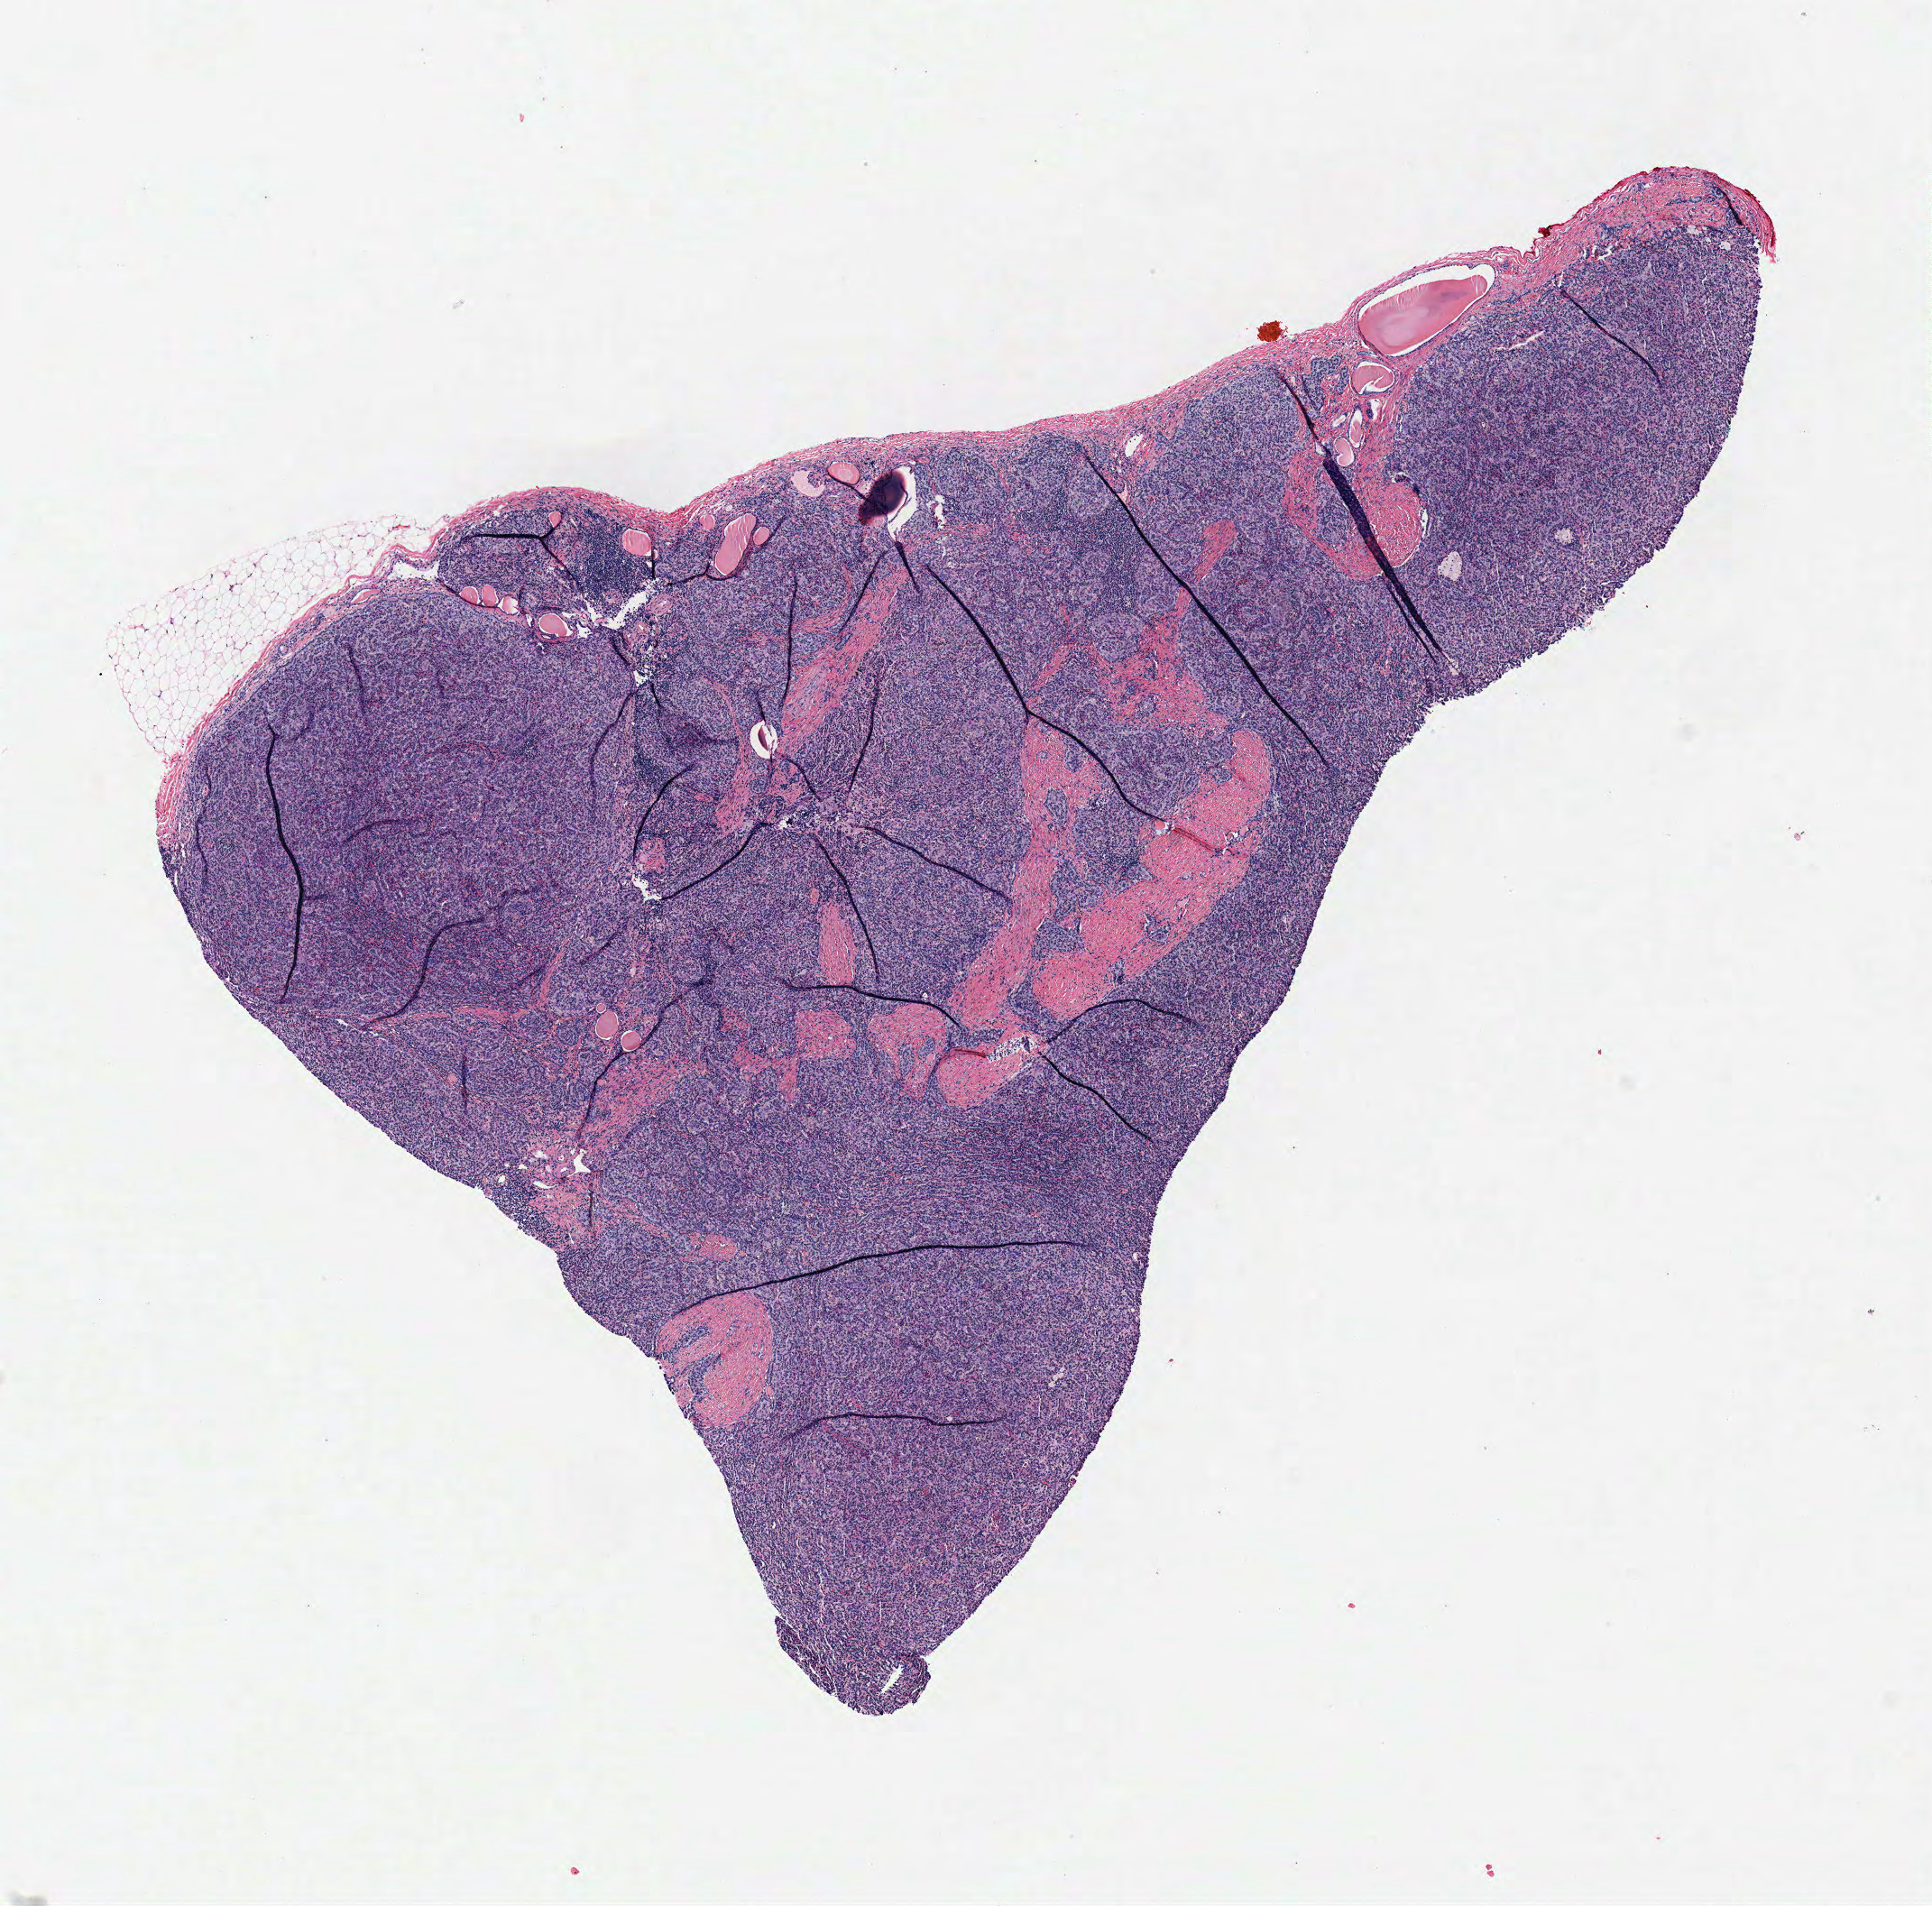
Digitized Hematoxylin and eosin (H&E) stained tissue section (whole slide), low-resolution overview of the scanned area, about 8.4 x 8.3 mm; frozen section from the top of the tissue portion; sample: primary tumour, kidney. Female, age 47 years at initial diagnosis. Pathologist review of this section (percent, as recorded): tumour cells 88%, tumour nuclei 80%, normal cells 0%, stromal cells 12%, necrosis 0%.
Histologic diagnosis: Papillary adenocarcinoma, NOS. AJCC pathologic stage: I (7th edition).